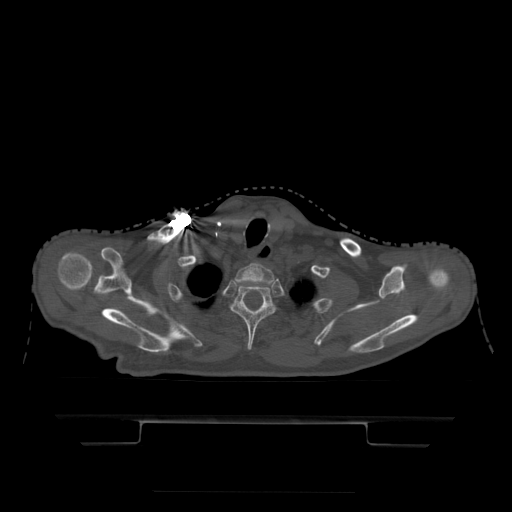
CT including the spine, one axial slice; slice 387 of 522 in the series (ordered by position); bone window (W 1800 / L 400 HU); 1.25 mm slice thickness; 512 × 512 image matrix, field of view 436 × 436 mm. Patient age 68 years. From the clinical record (not read from this slice): primary cancer: urothelial.
Outlined on this slice (semi-automatic segmentation, software-assisted and operator-edited):
- T1 vertebra: box from (x=234, y=264) to (x=275, y=284) px
- T2 vertebra: (x=232, y=284)–(x=275, y=351)